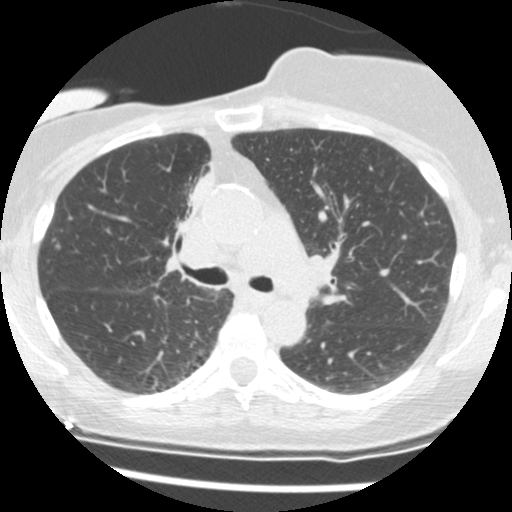
Axial slice from a low-dose chest CT screening exam. Second screening round (one year after baseline). Lung window (W 1500 / L -600 HU). 2.5 mm slice thickness. Slice 51 of 165 in the series. Female, age 56 years at enrolment. Current smoker at enrolment.
• Expert-annotated lung lesion, bounding box [x1, y1, x2, y2] px = [152, 170, 208, 261].
• The screening reader recorded 2 non-calcified nodules or masses ≥4 mm on this exam; which of them this box marks is not recorded.